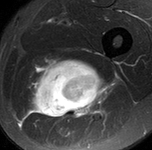
MRI of an extremity soft-tissue mass, one axial slice; position 78 of 90 along the scan axis; STIR; MR volume resampled by the dataset authors to the PET/CT grid (not the native acquisition matrix); 3.27 mm slice thickness; 152 × 150 image matrix, field of view 148 × 146 mm. Male patient. Case-level facts recorded for this patient, not image findings: histological type: undifferentiated pleomorphic liposarcoma; grade: high; site of the primary tumour: left thigh.
Outlined on this slice (expert contour drawn on MRI and transferred to this co-registered scan by the dataset authors):
- gross tumour volume including surrounding oedema: bounding box (x1, y1, x2, y2) in pixels: (25, 57, 113, 122)
- gross tumour volume (mass): (34, 60, 108, 117)